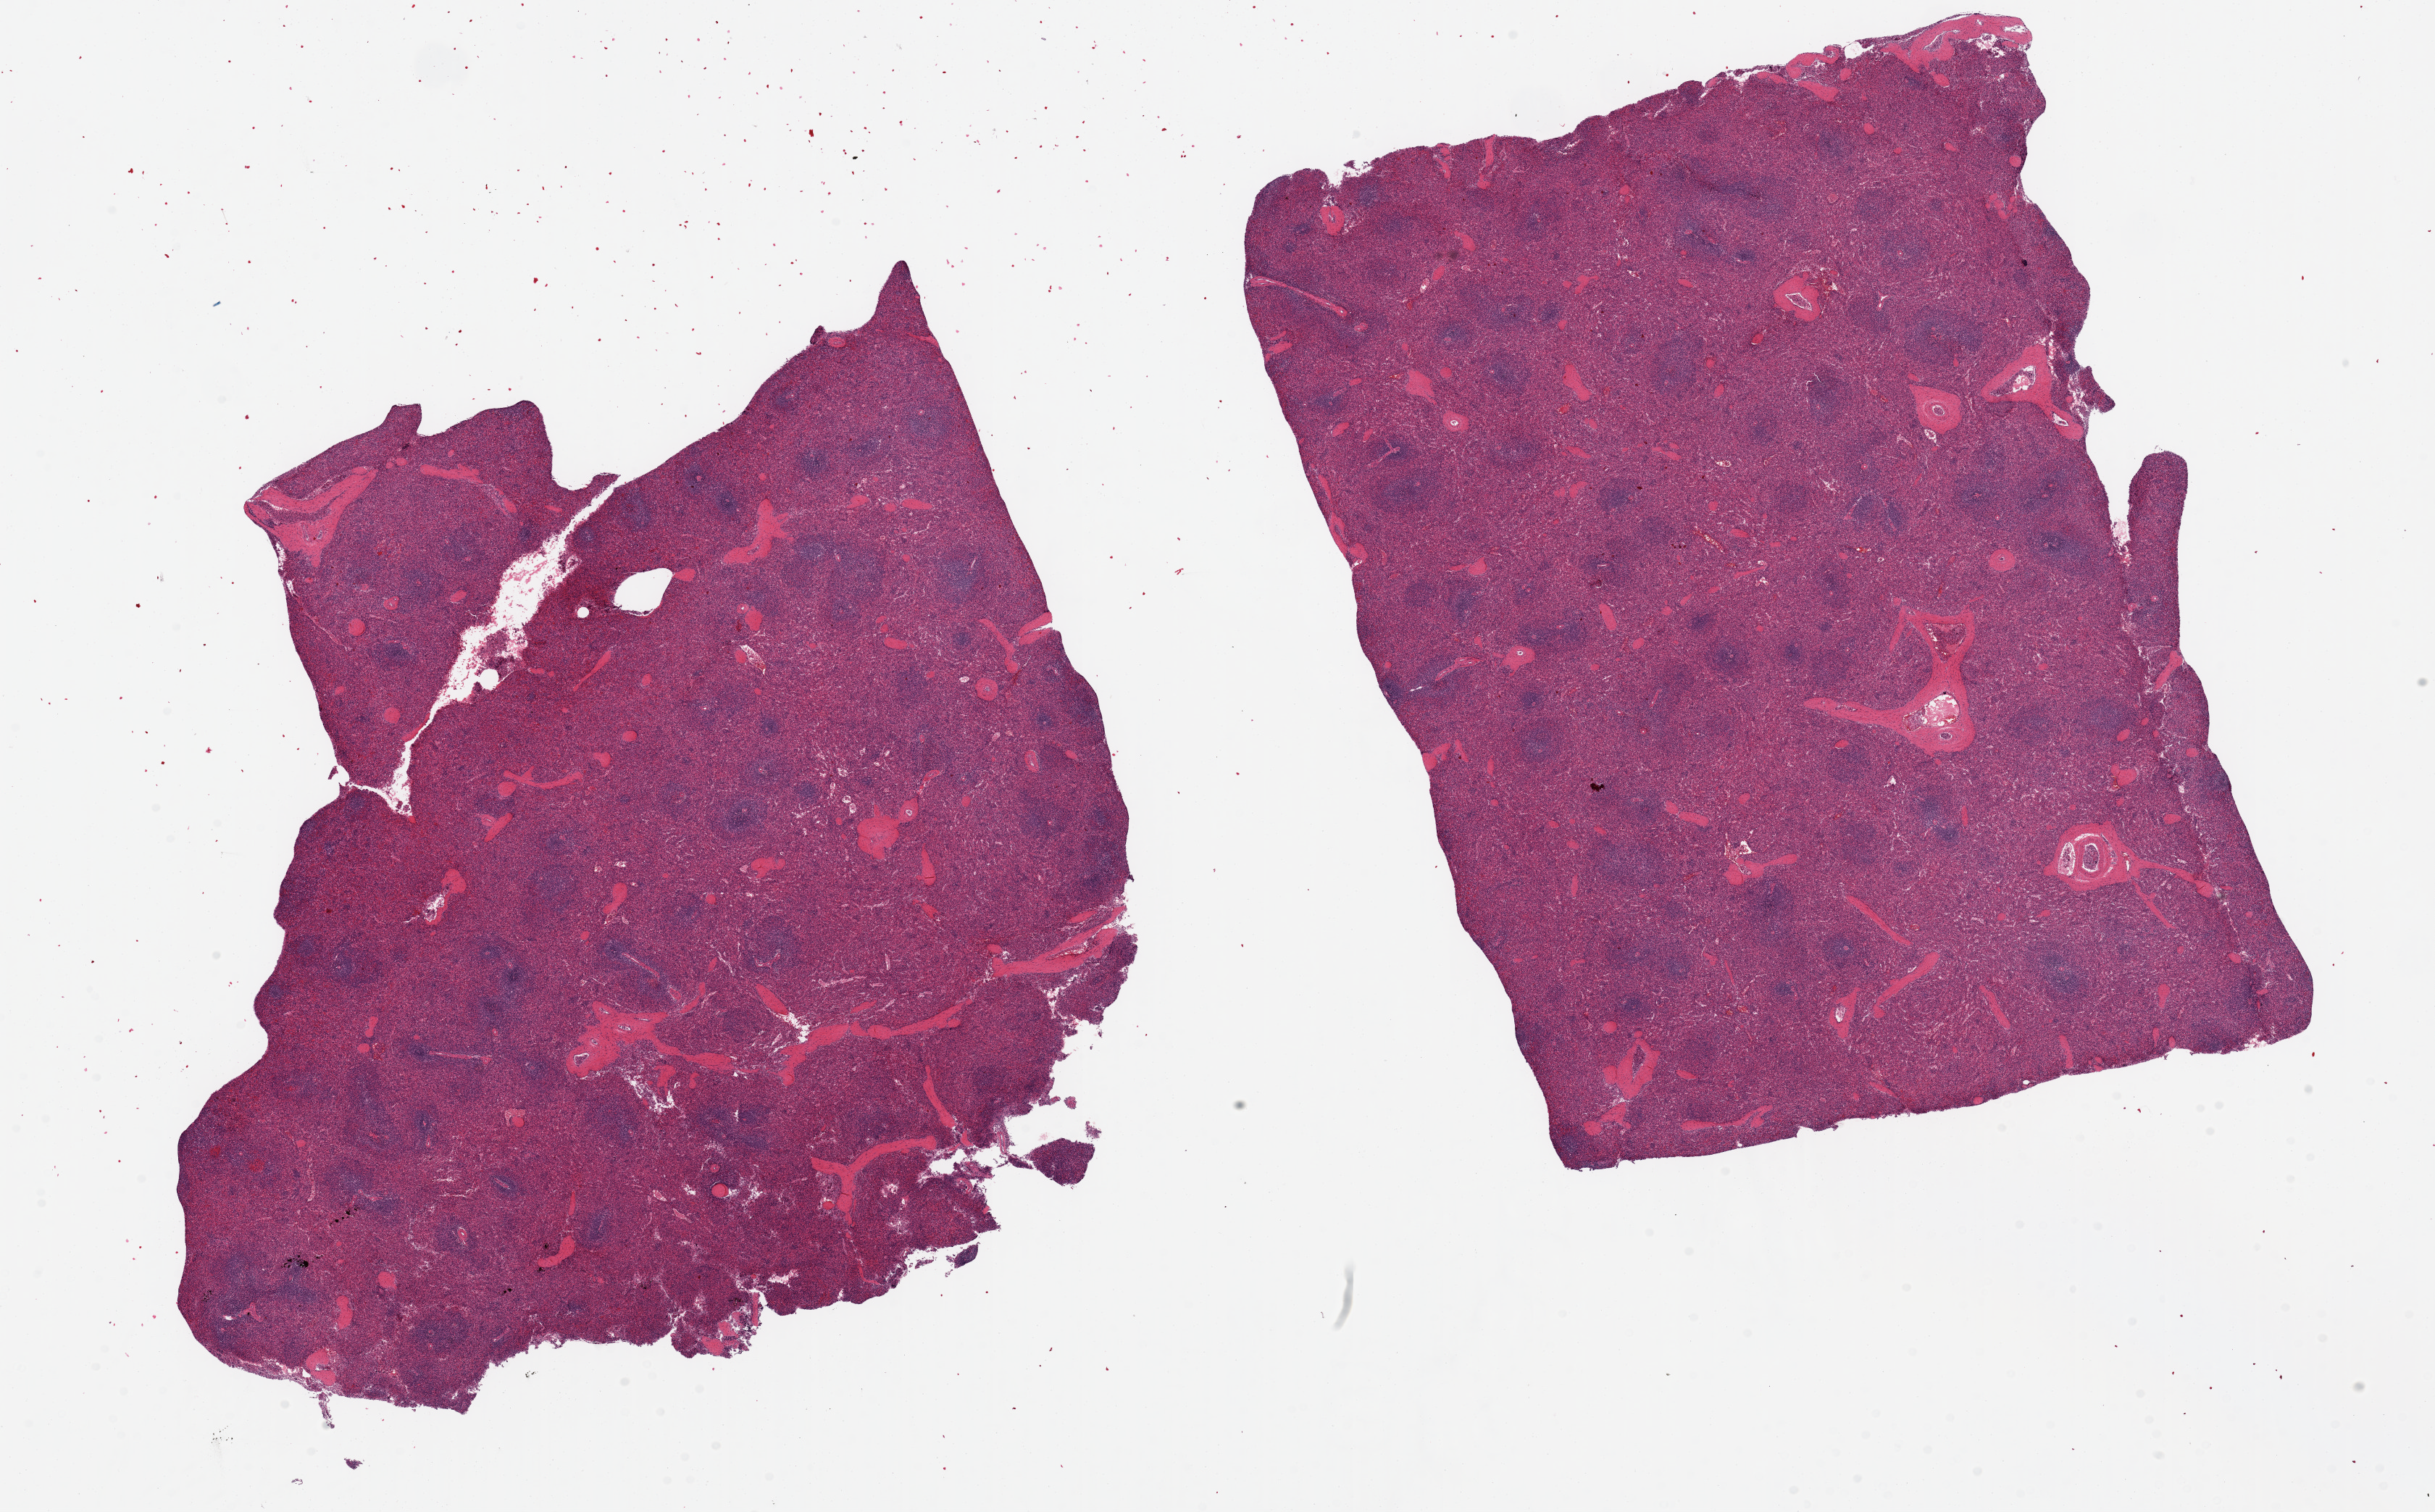
Haematoxylin and eosin whole-slide image, brightfield — whole scanned area (about 26.6 x 16.5 mm) shown as a low-resolution overview. PAXgene-fixed paraffin-embedded (PFPE) section. Section of spleen (target tissue). Donor tissue sample. Male donor.
Reviewer comment on this tissue sample: 2 aliquots, ~12x8mm.